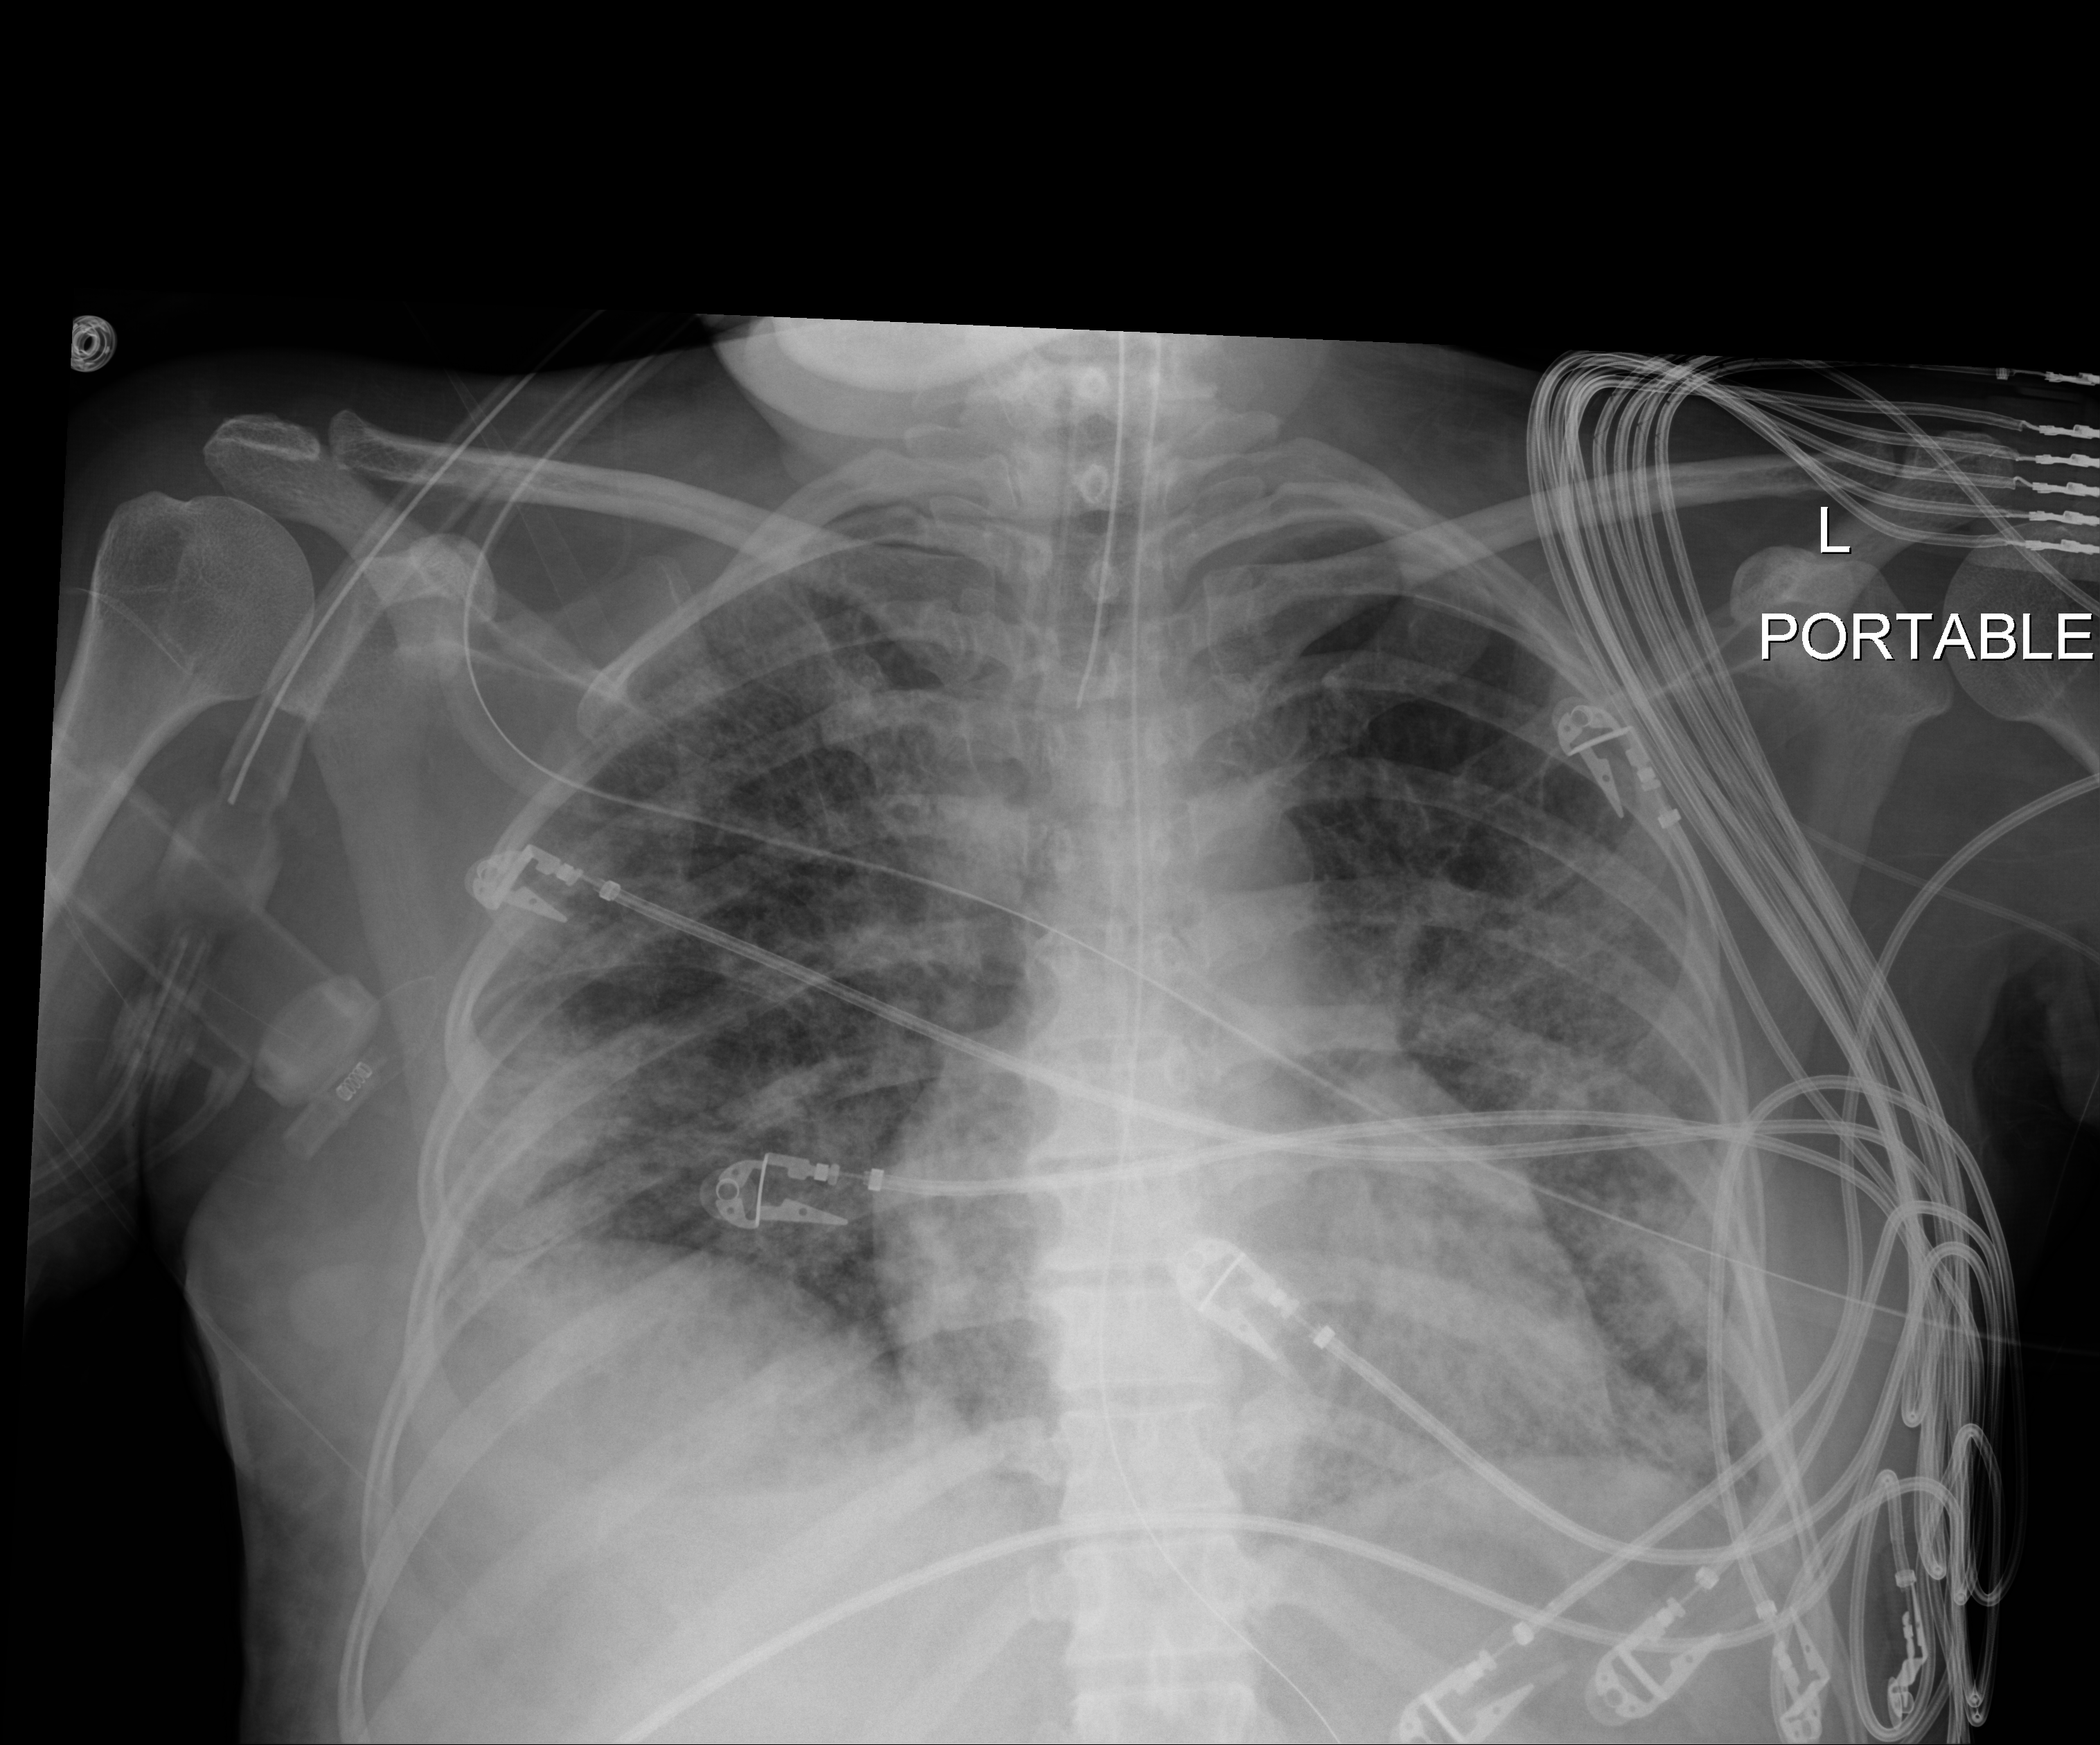
Portable chest radiograph, anteroposterior (AP) projection. Patient hospitalised with COVID-19; female, aged 18–59 years.
Hospital-stay facts (about this admission, not read from this image; timing relative to this image not recorded): mechanically ventilated during this hospital stay: yes; other chronic lung disease (admission record): no.